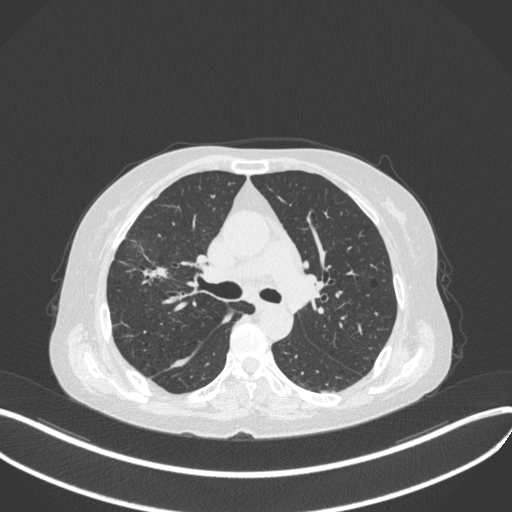
Chest CT, one axial slice; slice 254 of 429 in the series (ordered by position); reconstruction kernel B31f; 120 kVp; lung window (W 1500 / L -600 HU); 1 mm slice thickness; 512 × 512 image matrix, field of view 400 × 400 mm. Female patient, age 69 years. From the clinical record (not read from this slice): clinical TNM (as recorded): T1b N3 M0.
Outlined on this slice (rectangle marked by the reading radiologist):
- lung tumour (recorded histology: small cell carcinoma): box from (x=136, y=253) to (x=176, y=285) px